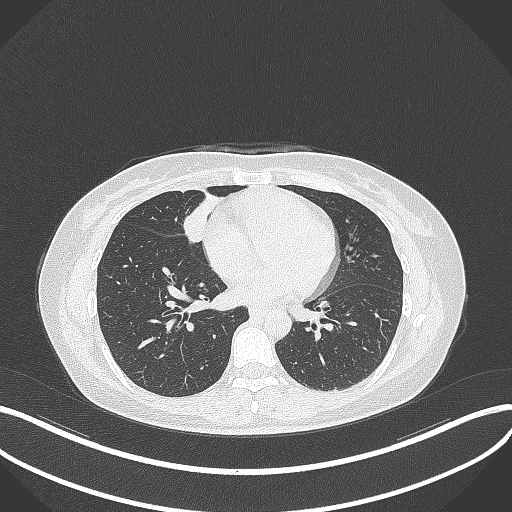
Chest CT, one axial slice. Slice 116 of 284 in the series (ordered by position). Reconstruction kernel B70f. 120 kVp. Lung window (W 1500 / L -600 HU). 1 mm slice thickness. 512 × 512 image matrix, field of view 400 × 400 mm. Patient: female, 43 years. From the clinical record (not read from this slice): clinical TNM (as recorded): T1c N3 M1; histopathological grade: G1.
Annotated regions visible in this slice (rectangle marked by the reading radiologist):
- lung tumour (recorded histology: adenocarcinoma): bounding box <180,200,214,250> (left, top, right, bottom; pixels)